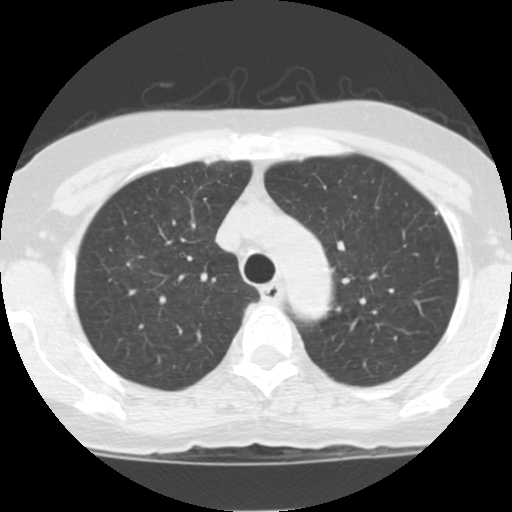
Chest CT (low-dose screening protocol), one axial image, second annual screen, lung window (W 1500 / L -600 HU), 2.5 mm slice thickness, slice 27 of 118 in the series, 512 × 512 image matrix, field of view 290 × 290 mm. Female participant, aged 62 years at enrolment. Current smoker at enrolment.
Expert reader's lesion annotation, bounding box <110,242,152,286> (left, top, right, bottom; pixels). The exam's reader record, not a measurement of the box and not confirmed to be the same lesion: non-calcified nodule or mass ≥4 mm, right upper lobe, 8 × 7 mm, poorly defined margins, ground glass attenuation, pre-existing on the prior screen: yes; interval growth: yes. Official screen result: positive, other. Later outcome: lung cancer diagnosed 433 days after this screen — bronchiolo-alveolar adenocarcinoma, NOS, right upper lobe, stage IA (AJCC 6th edition), 10 mm at pathology.